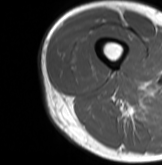
MRI of an extremity soft-tissue mass, one axial slice. Position 15 of 61 along the scan axis. MR volume resampled by the dataset authors to the PET/CT grid (not the native acquisition matrix). 3.27 mm slice thickness. 162 × 165 image matrix. Male patient. From the clinical record (not read from this slice): histological type: poorly differentiated synovial sarcoma; grade: high; site of the primary tumour: right buttock.
Annotated regions visible in this slice (expert contour drawn on MRI and transferred to this co-registered scan by the dataset authors):
- gross tumour volume including surrounding oedema: box from (x=61, y=47) to (x=95, y=82) px